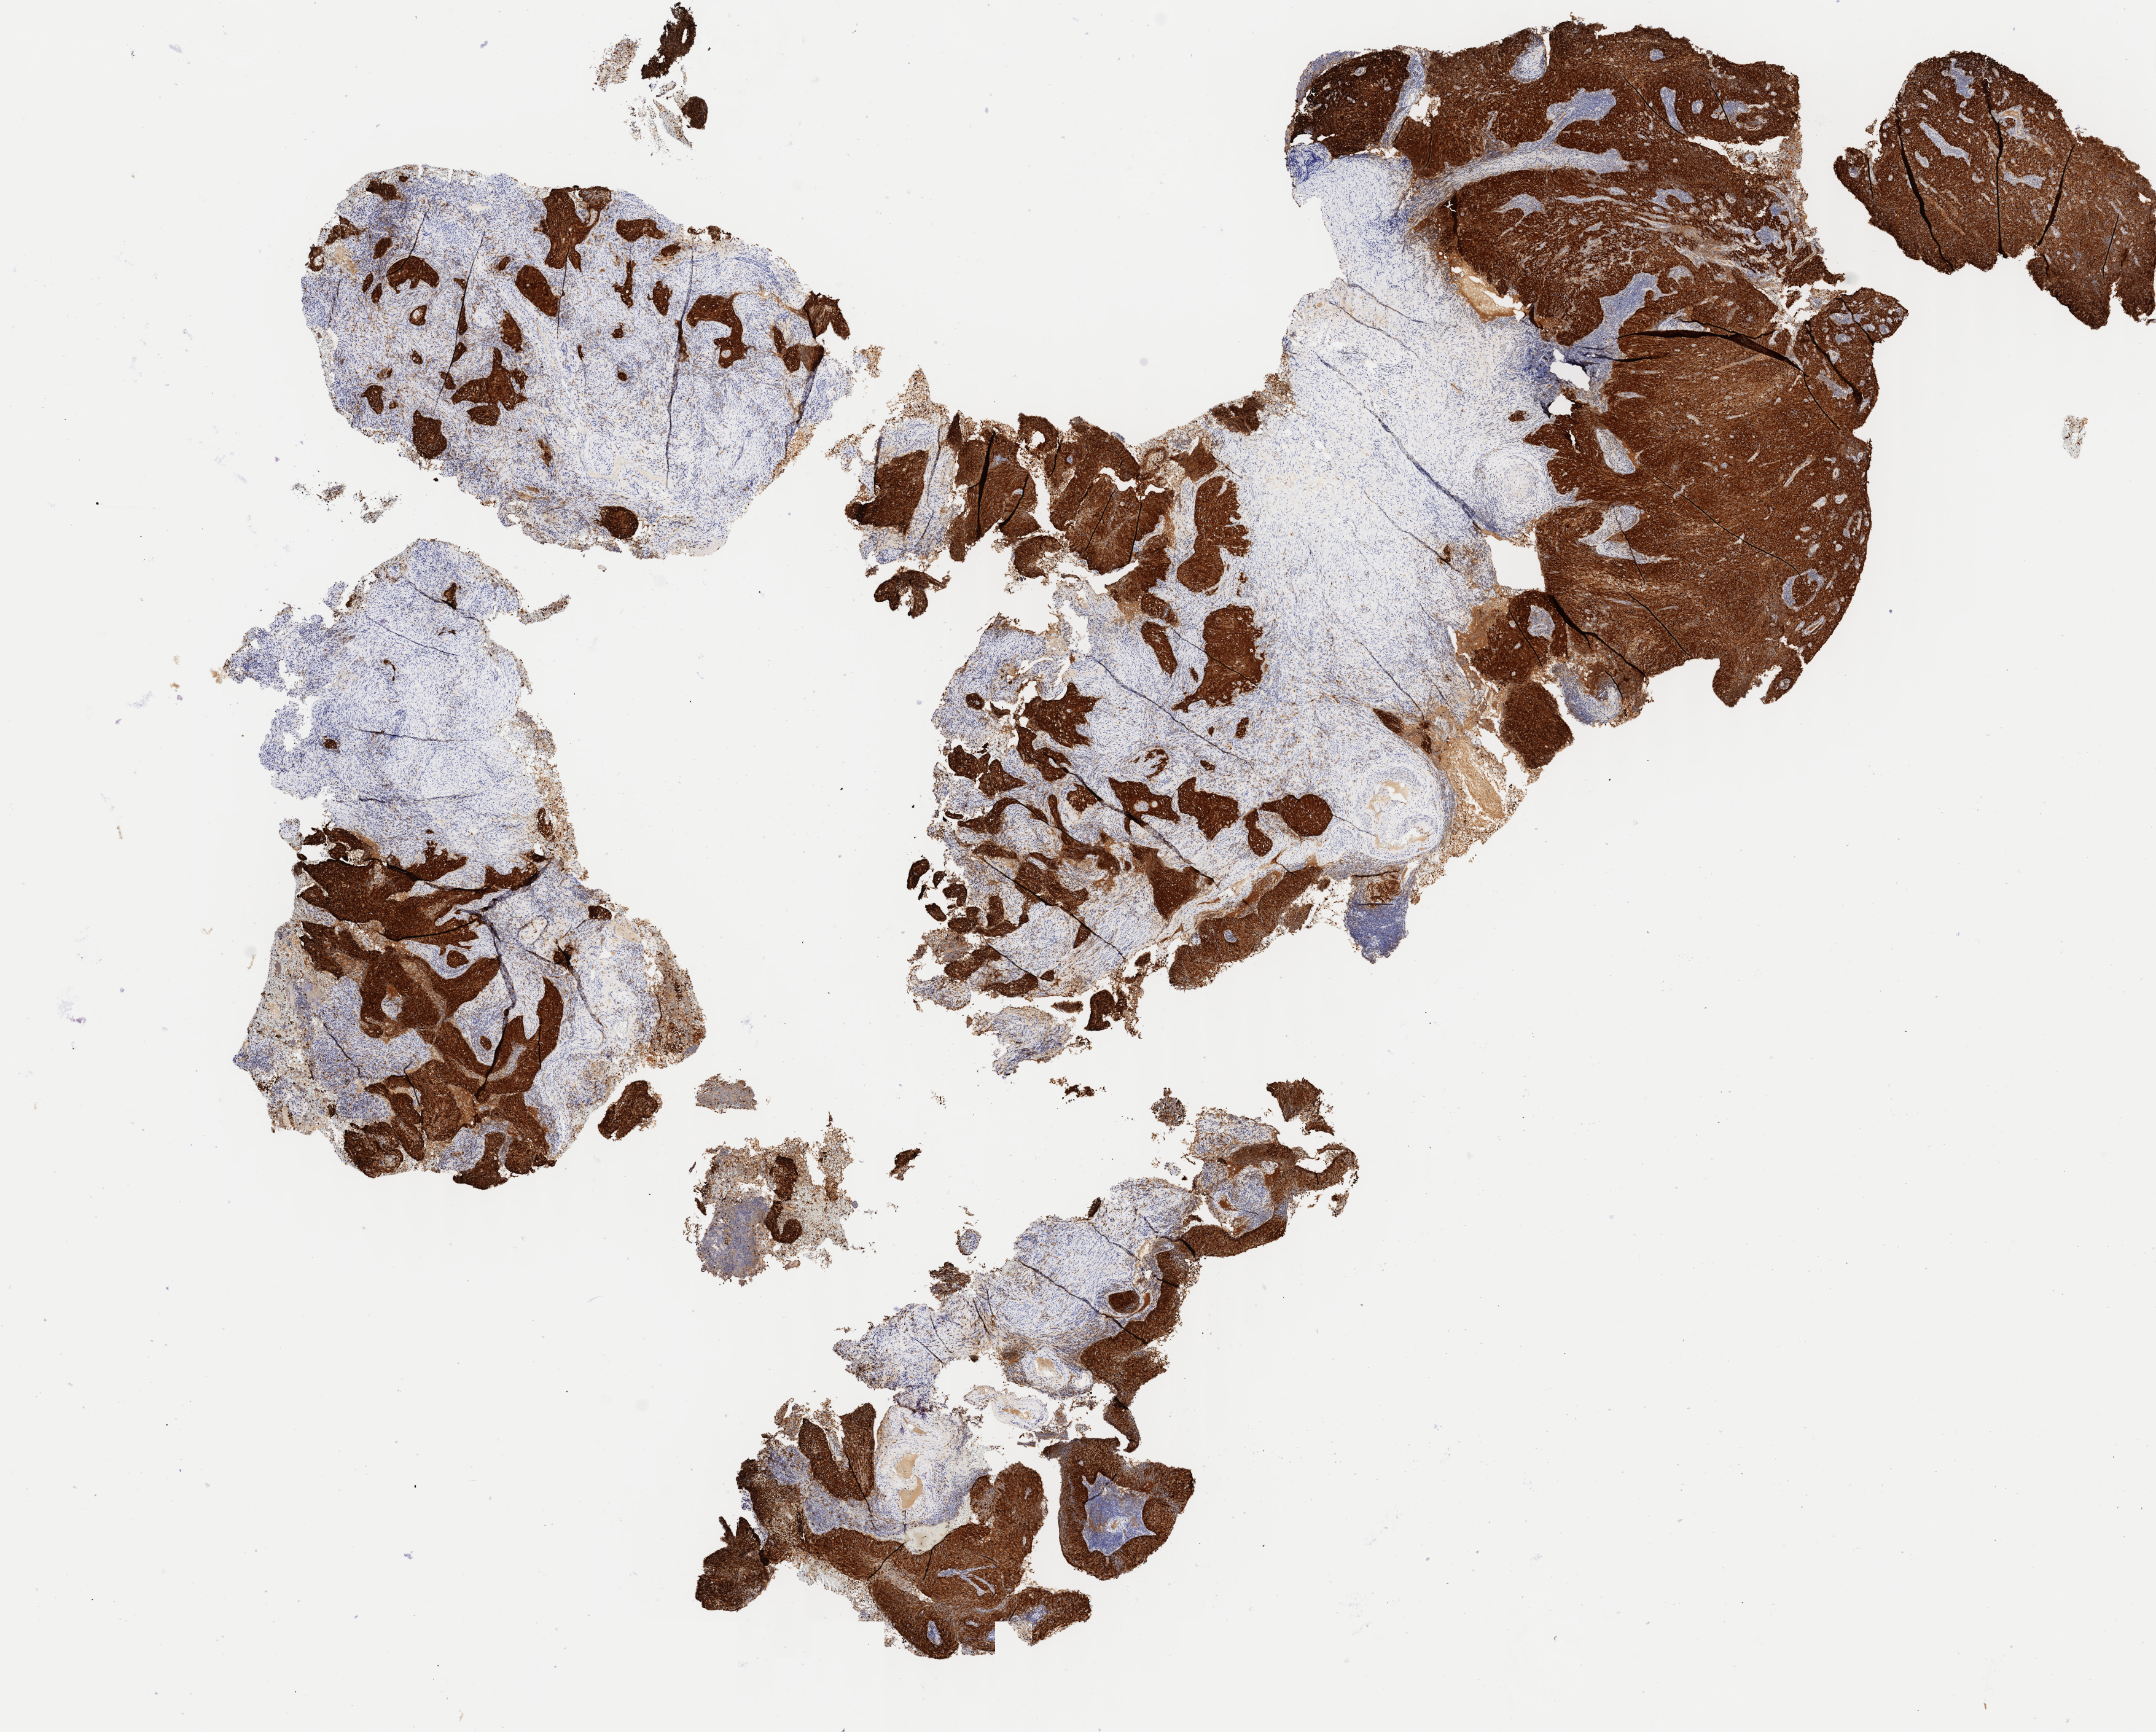
Immunohistochemistry (IHC) whole-slide image stained for p16 (p16INK4a), a low-resolution overview of the entire scanned area, about 14.0 x 11.2 mm, tumor tissue, site: cervix. Patient female; age 62 years.
- diagnosis: Squamous cell carcinoma, large cell, nonkeratinizing, NOS